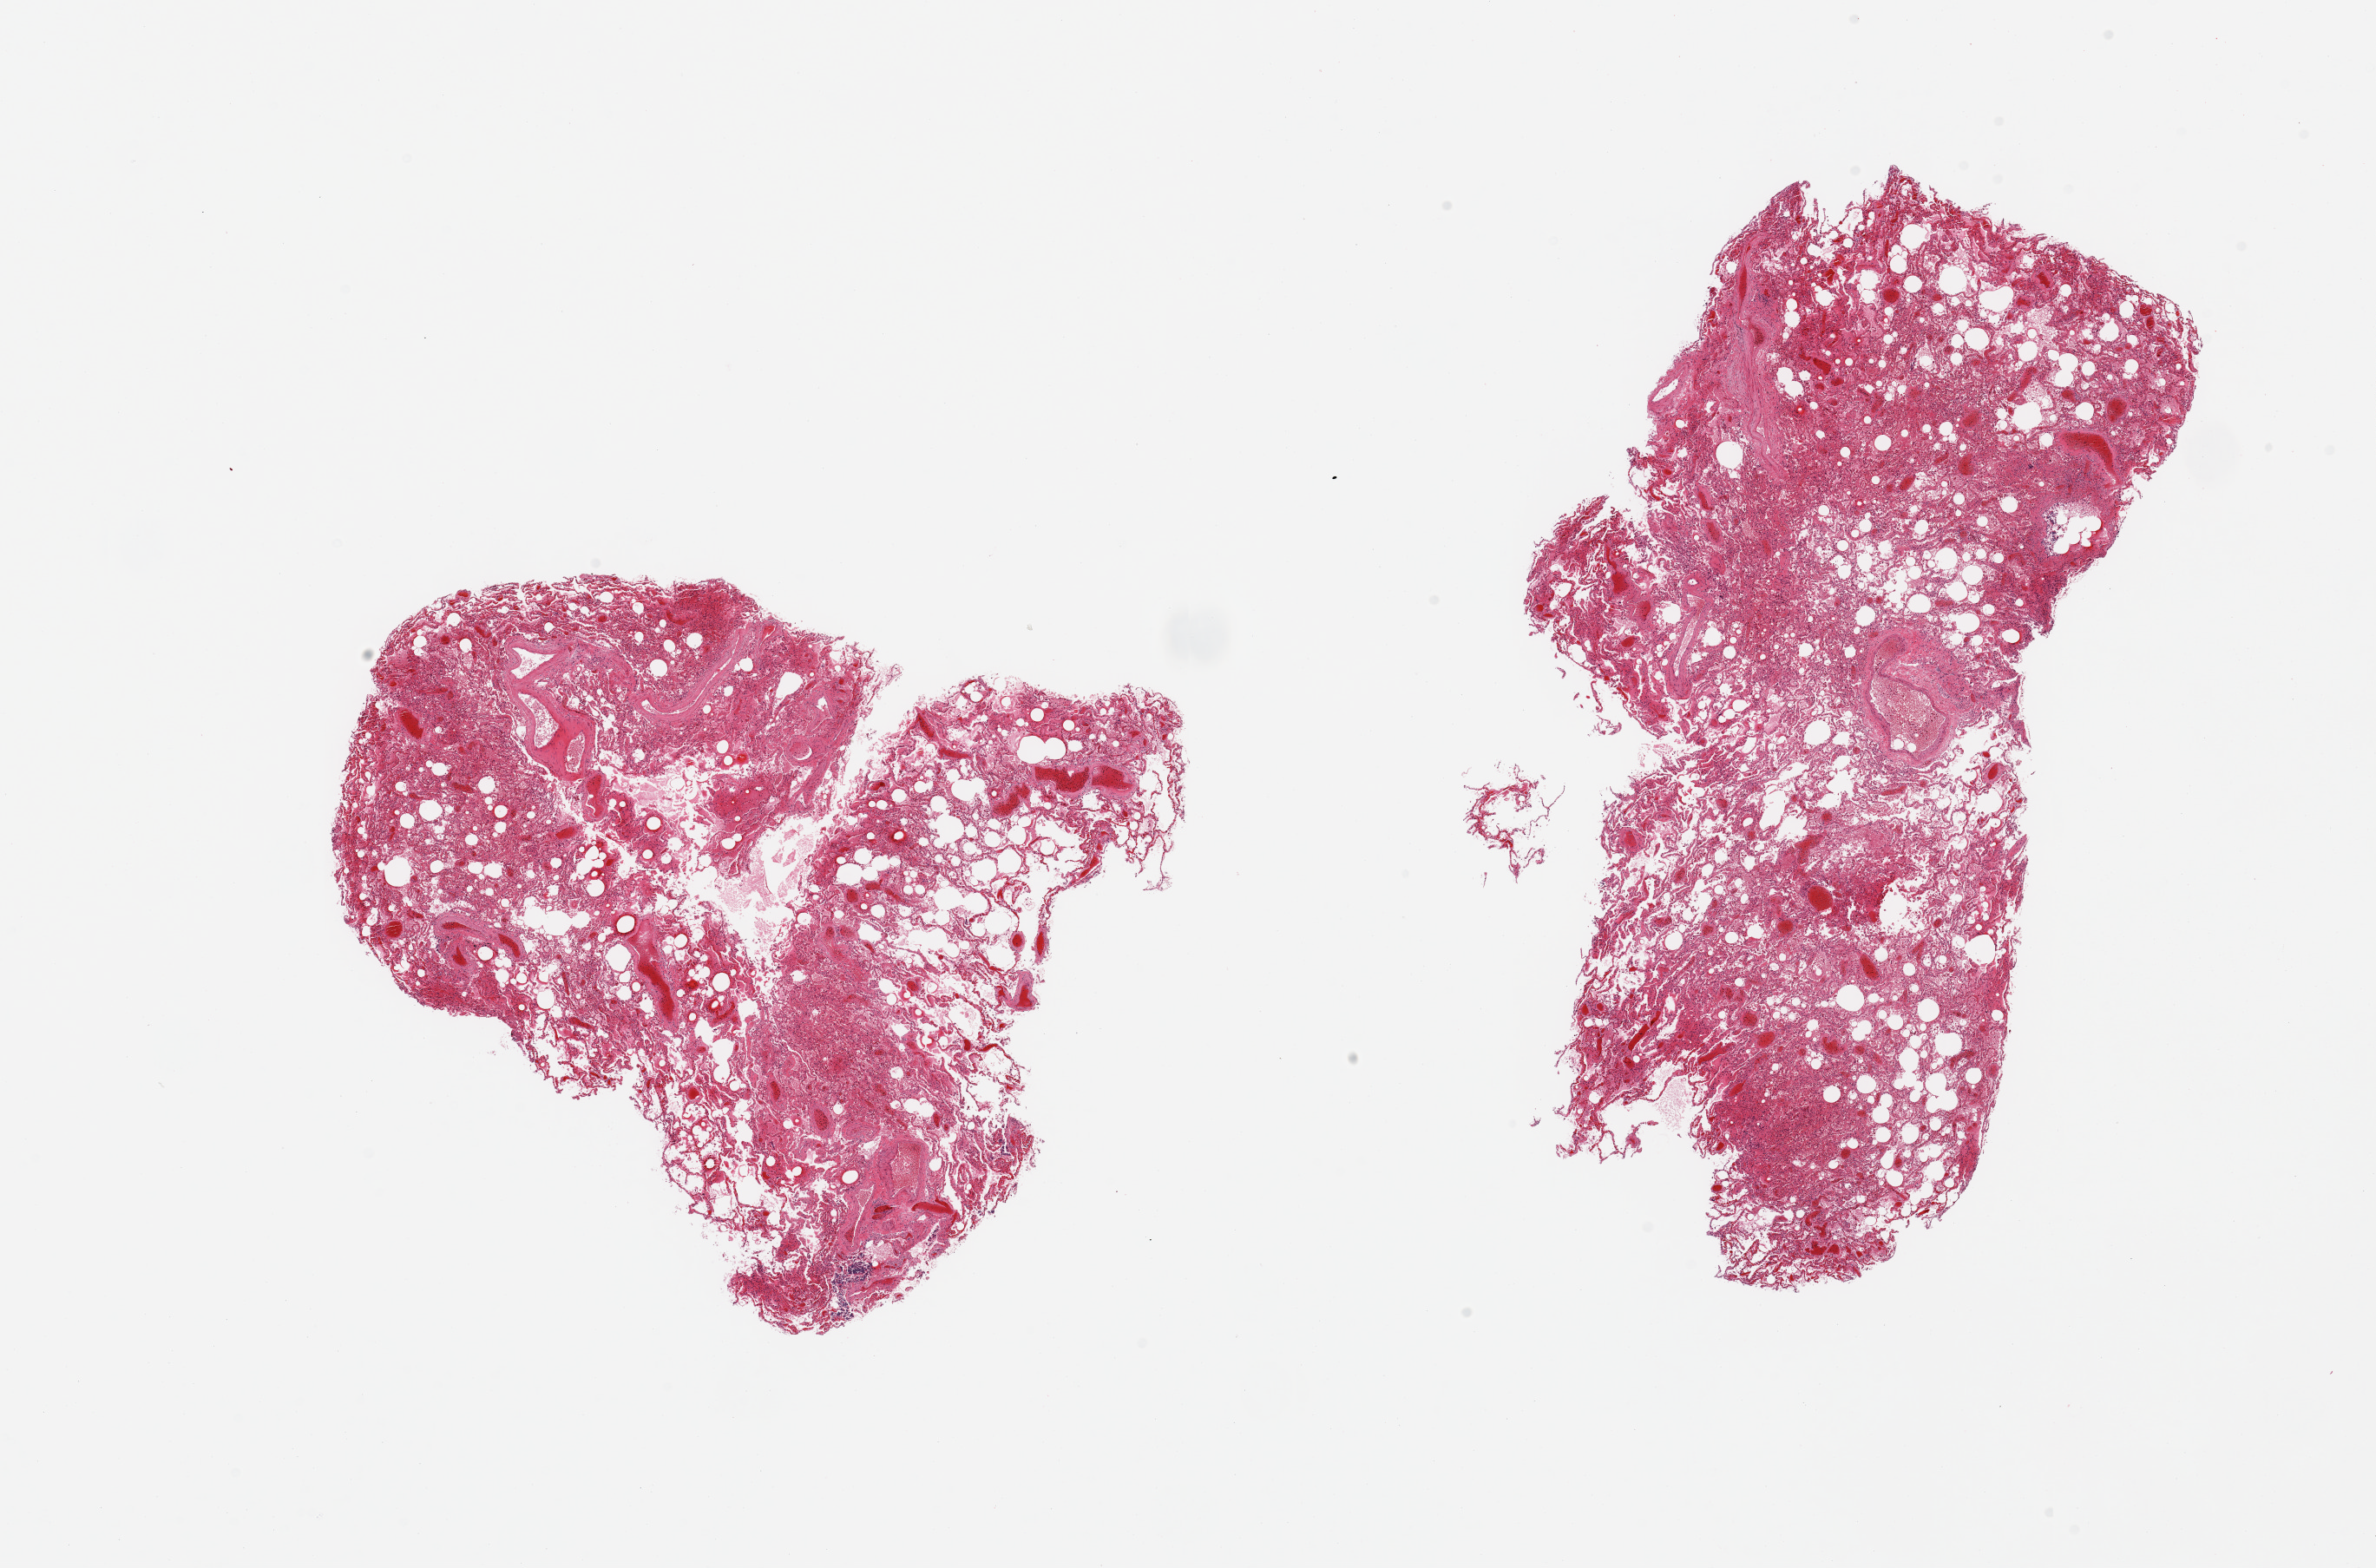
Digitized haematoxylin and eosin-stained section — whole scanned area (about 21.7 x 14.3 mm) shown as a low-resolution overview, PAXgene-fixed paraffin-embedded (PFPE) section, section of lung (target tissue), tissue donor sample. Donor sex: male.
Review note (as recorded): 2 pieces. moderate congestion/atatlectasis.